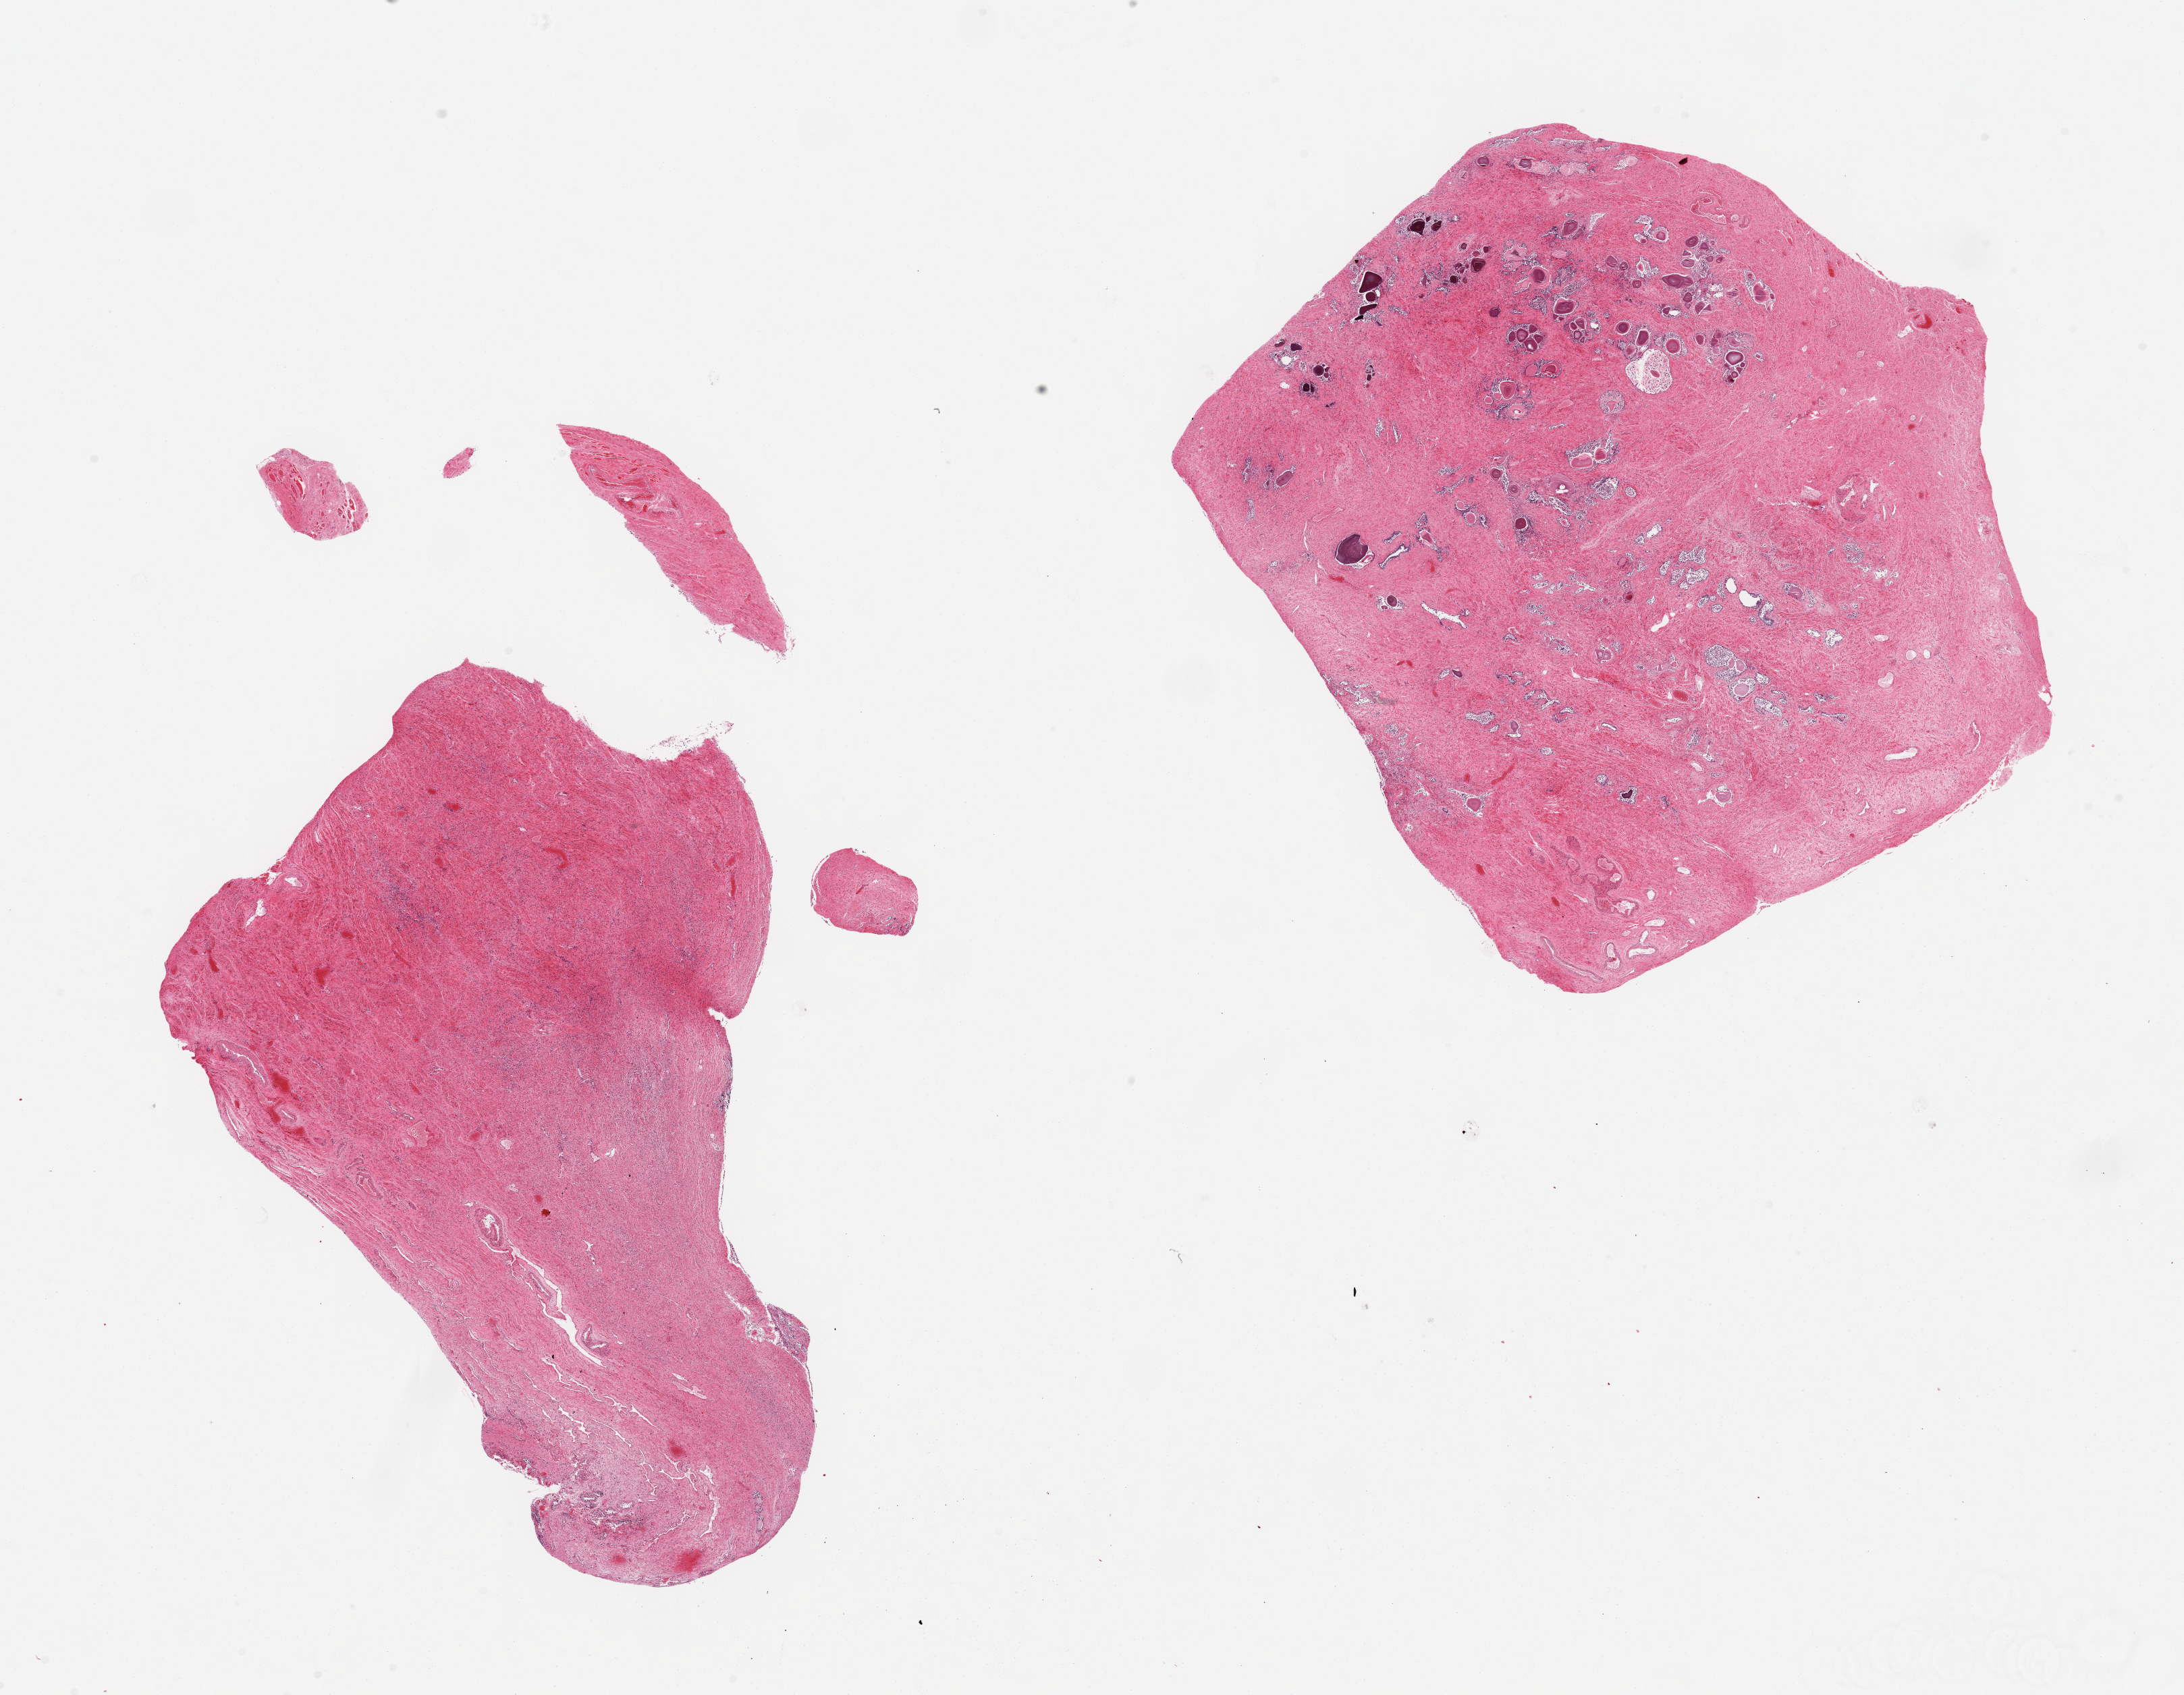
Digitized haematoxylin and eosin-stained section, brightfield — whole scanned area (about 25.6 x 19.9 mm) shown as a low-resolution overview. PAXgene-fixed, paraffin-embedded tissue. Sampled site (target tissue): prostate. Tissue donor sample. Donor sex: male.
Pathologist's review note for this sample: 2 pieces; glands autolyzed; stroma, which is predominant, intact.